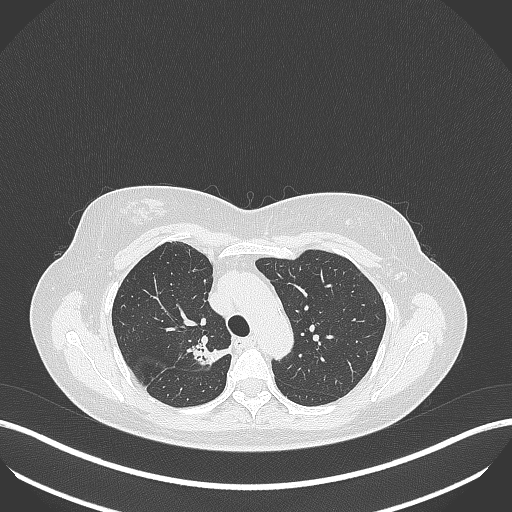
Chest CT, one axial slice. Position 286 of 386 along the scan axis. Reconstruction kernel B70f. Lung window (W 1500 / L -600 HU). 1 mm slice thickness. 512 × 512 image matrix, field of view 400 × 400 mm. Patient: female, 65 years. From the clinical record (not read from this slice): clinical TNM (as recorded): T1b N0 M0.
Outlined on this slice (bounding box drawn by a radiologist):
- lung tumour (recorded histology: adenocarcinoma): bounding box (x1, y1, x2, y2) in pixels: (190, 335, 232, 370)